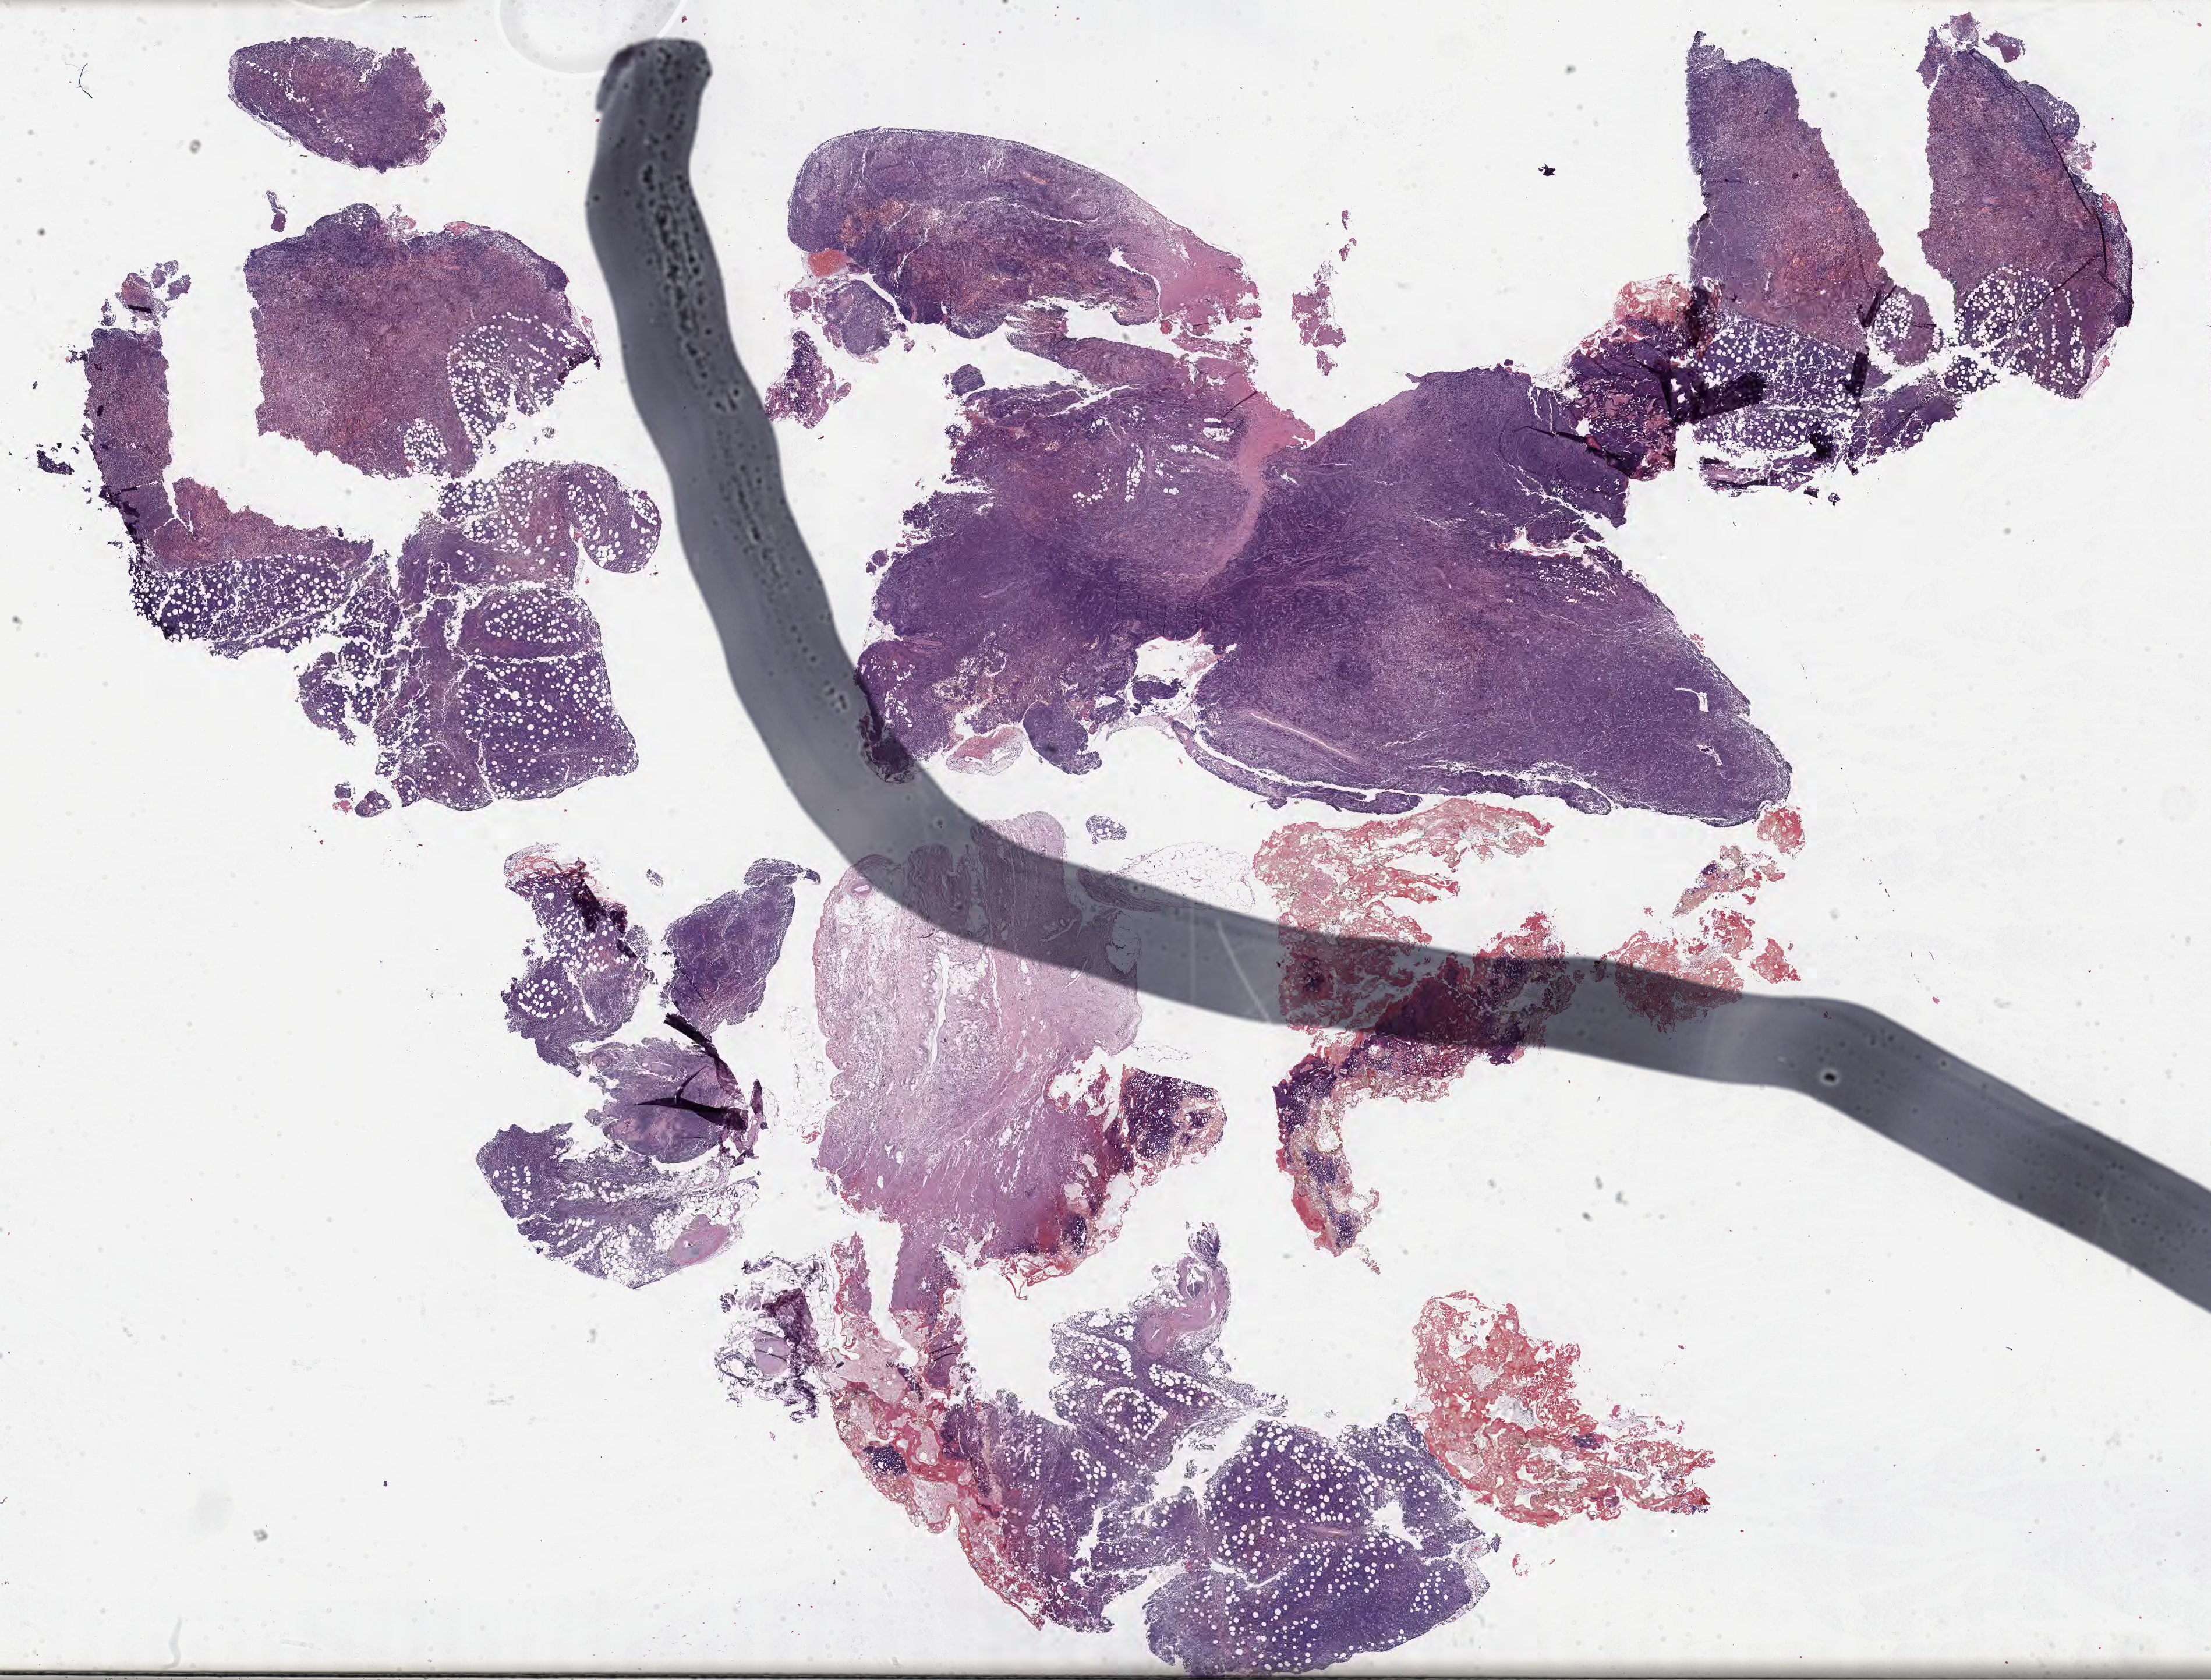
Digitized H&E-stained section — whole scanned area (about 30.7 x 23.3 mm) shown as a low-resolution overview; specimen: tumor tissue. Female patient, aged 72.
Histologic diagnosis: Burkitt lymphoma, NOS.